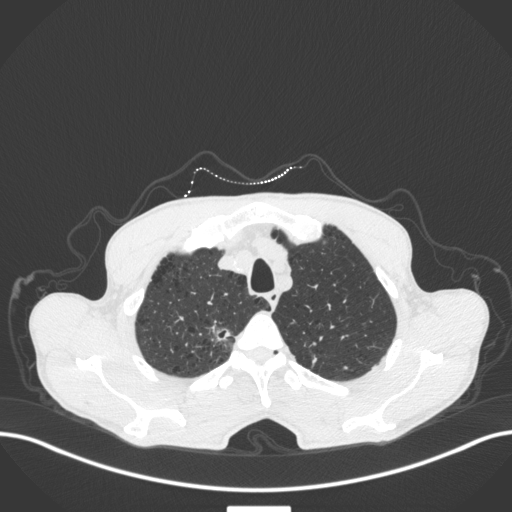
Chest CT, one axial slice. Slice 365 of 445 in the series (ordered by position). Reconstruction kernel B31f. Lung window (W 1500 / L -600 HU). 1 mm slice thickness. 512 × 512 image matrix, field of view 400 × 400 mm. Male patient, age 70 years. Case-level facts recorded for this patient, not image findings: clinical TNM (as recorded): T1a N0 M0; histopathological grade: G1-2.
Annotated regions visible in this slice (rectangle marked by the reading radiologist):
- lung tumour (recorded histology: adenocarcinoma): box from (x=205, y=319) to (x=233, y=346) px